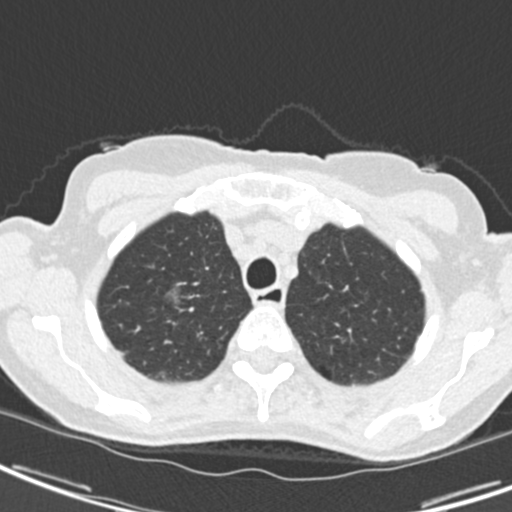
Low-dose screening chest CT, one axial slice; position 165 of 189 along the scan axis; reconstruction kernel B30f; 120 kVp; lung window (W 1500 / L -600 HU); 2 mm slice thickness; 512 × 512 image matrix, field of view 279 × 279 mm.
Annotated regions visible in this slice (outlined manually by an expert reader):
- lesion 1 (tumor, upper lobe of right lung): bounding box (x1, y1, x2, y2) in pixels: (165, 286, 184, 308)